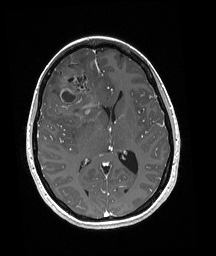
Brain MRI from a brain-tumour surgery series, one axial slice; slice 93 of 192 in the series (ordered by position); T1-weighted post-contrast; 216 × 256 image matrix, field of view 211 × 250 mm. Case-level facts recorded for this patient, not image findings: histopathology: Oligodendroglioma; WHO grade: 3; IDH mutation: yes.
Structures marked on this image (manually delineated by an expert):
- tumour: bounding box [x1, y1, x2, y2] px = [50, 61, 98, 120]